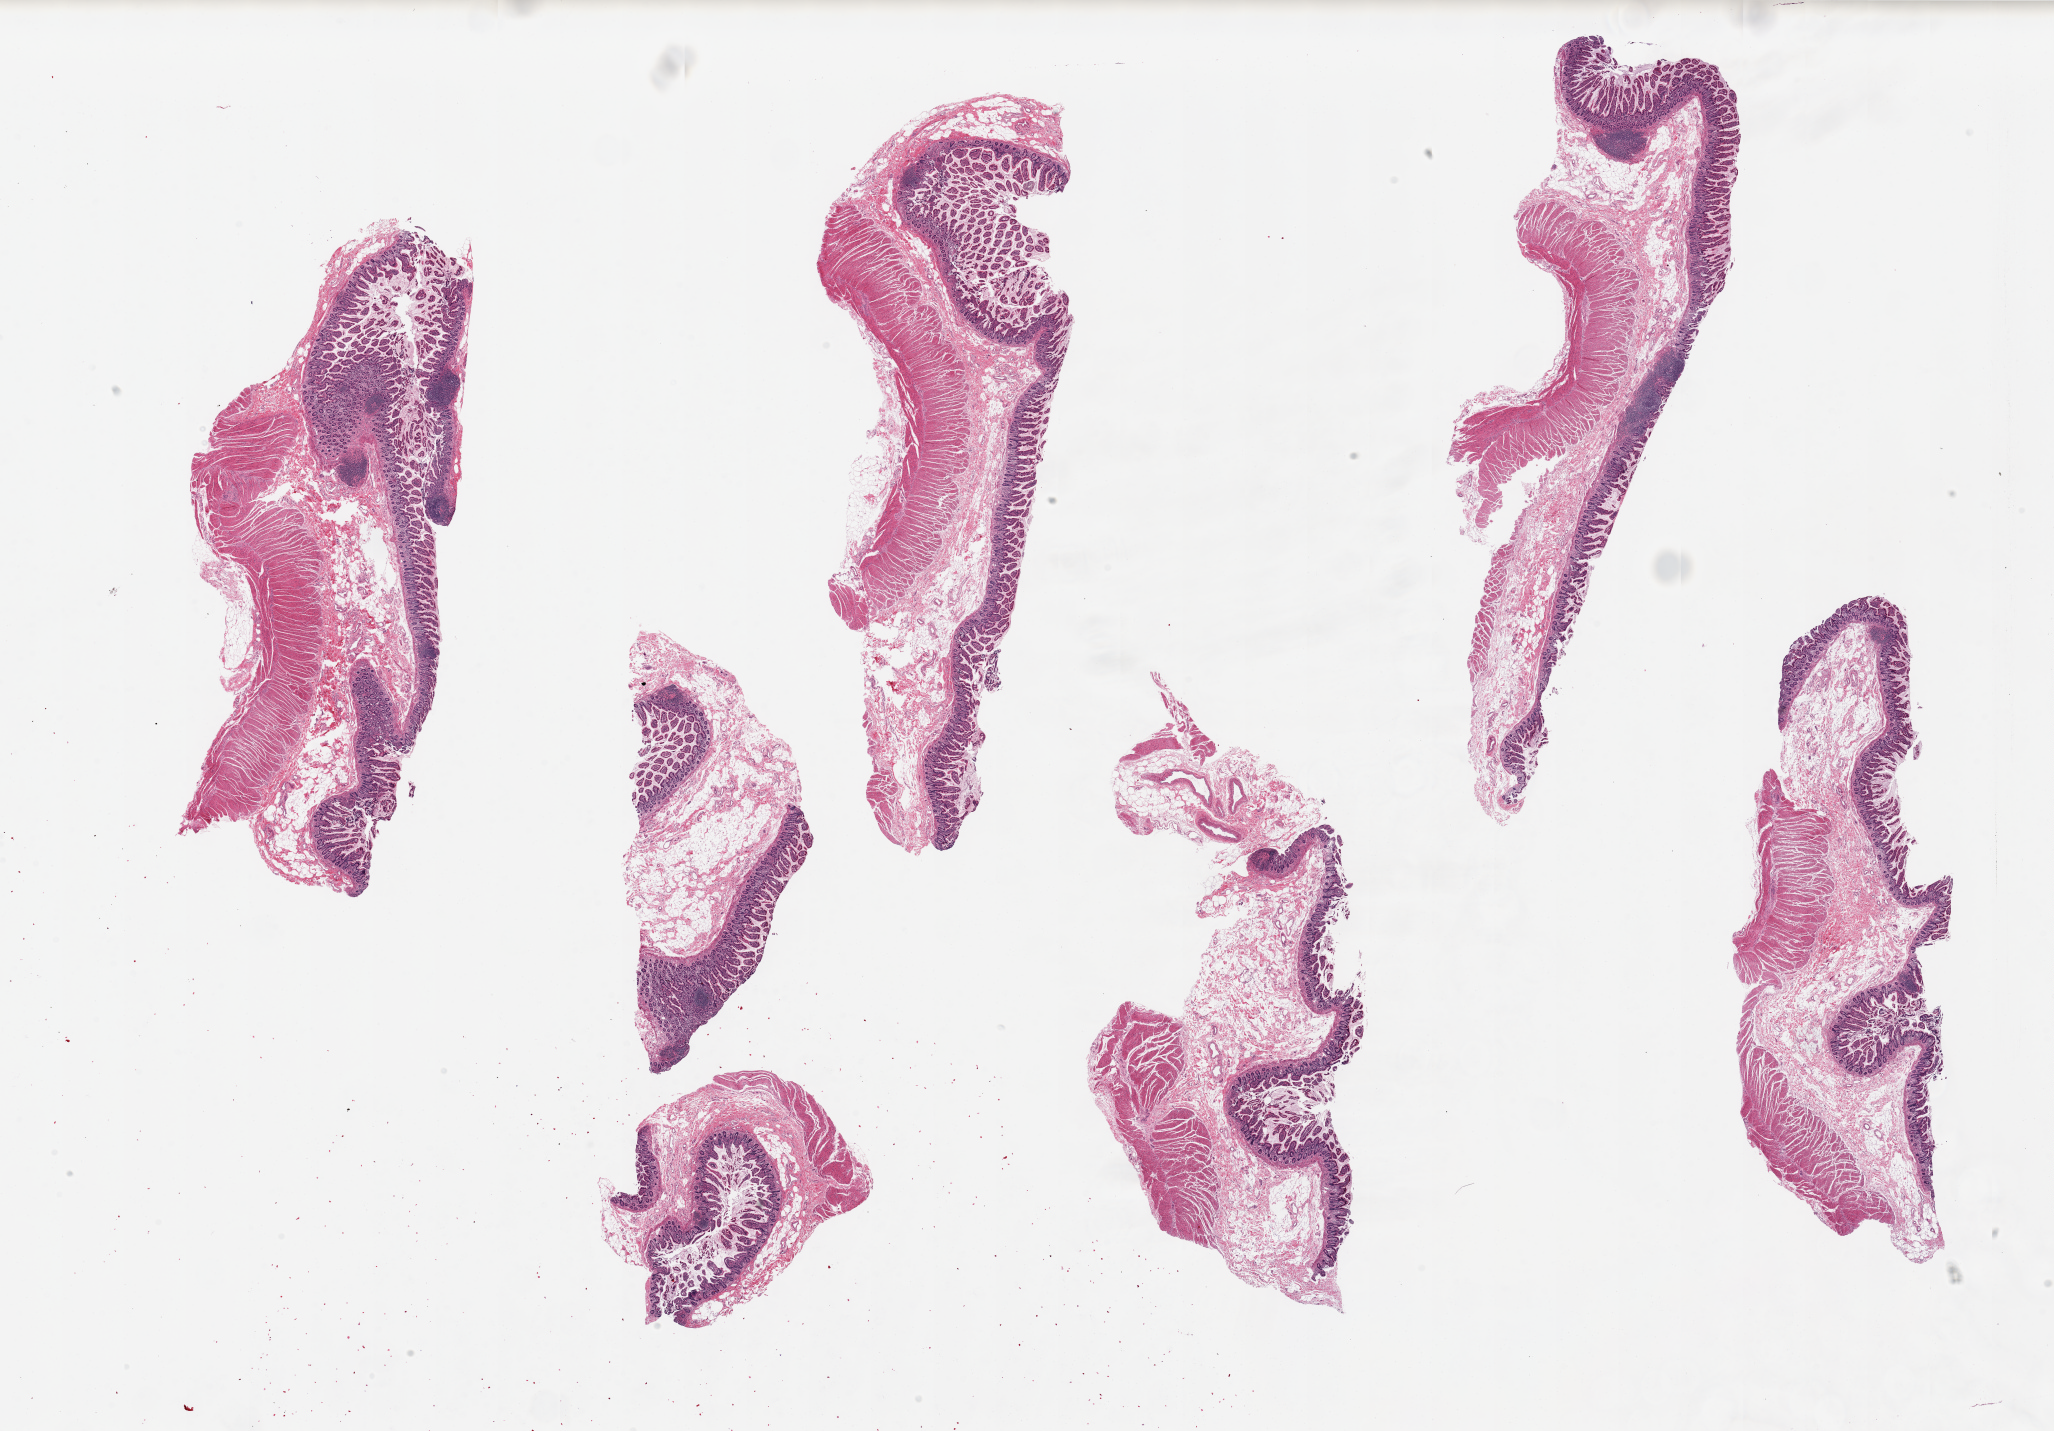
Haematoxylin and eosin whole-slide image, brightfield, whole scanned area (about 32.5 x 22.6 mm, from a 20x scan) shown as a low-resolution overview. PAXgene-fixed, paraffin-embedded tissue. Target tissue: ileum. Donor tissue sample. Donor: male.
Review note (as recorded): 6 pieces, up to 13x4mm; 5 of 6 pieces contain both mucosa and muscularis; Lymphoid tissue on image.